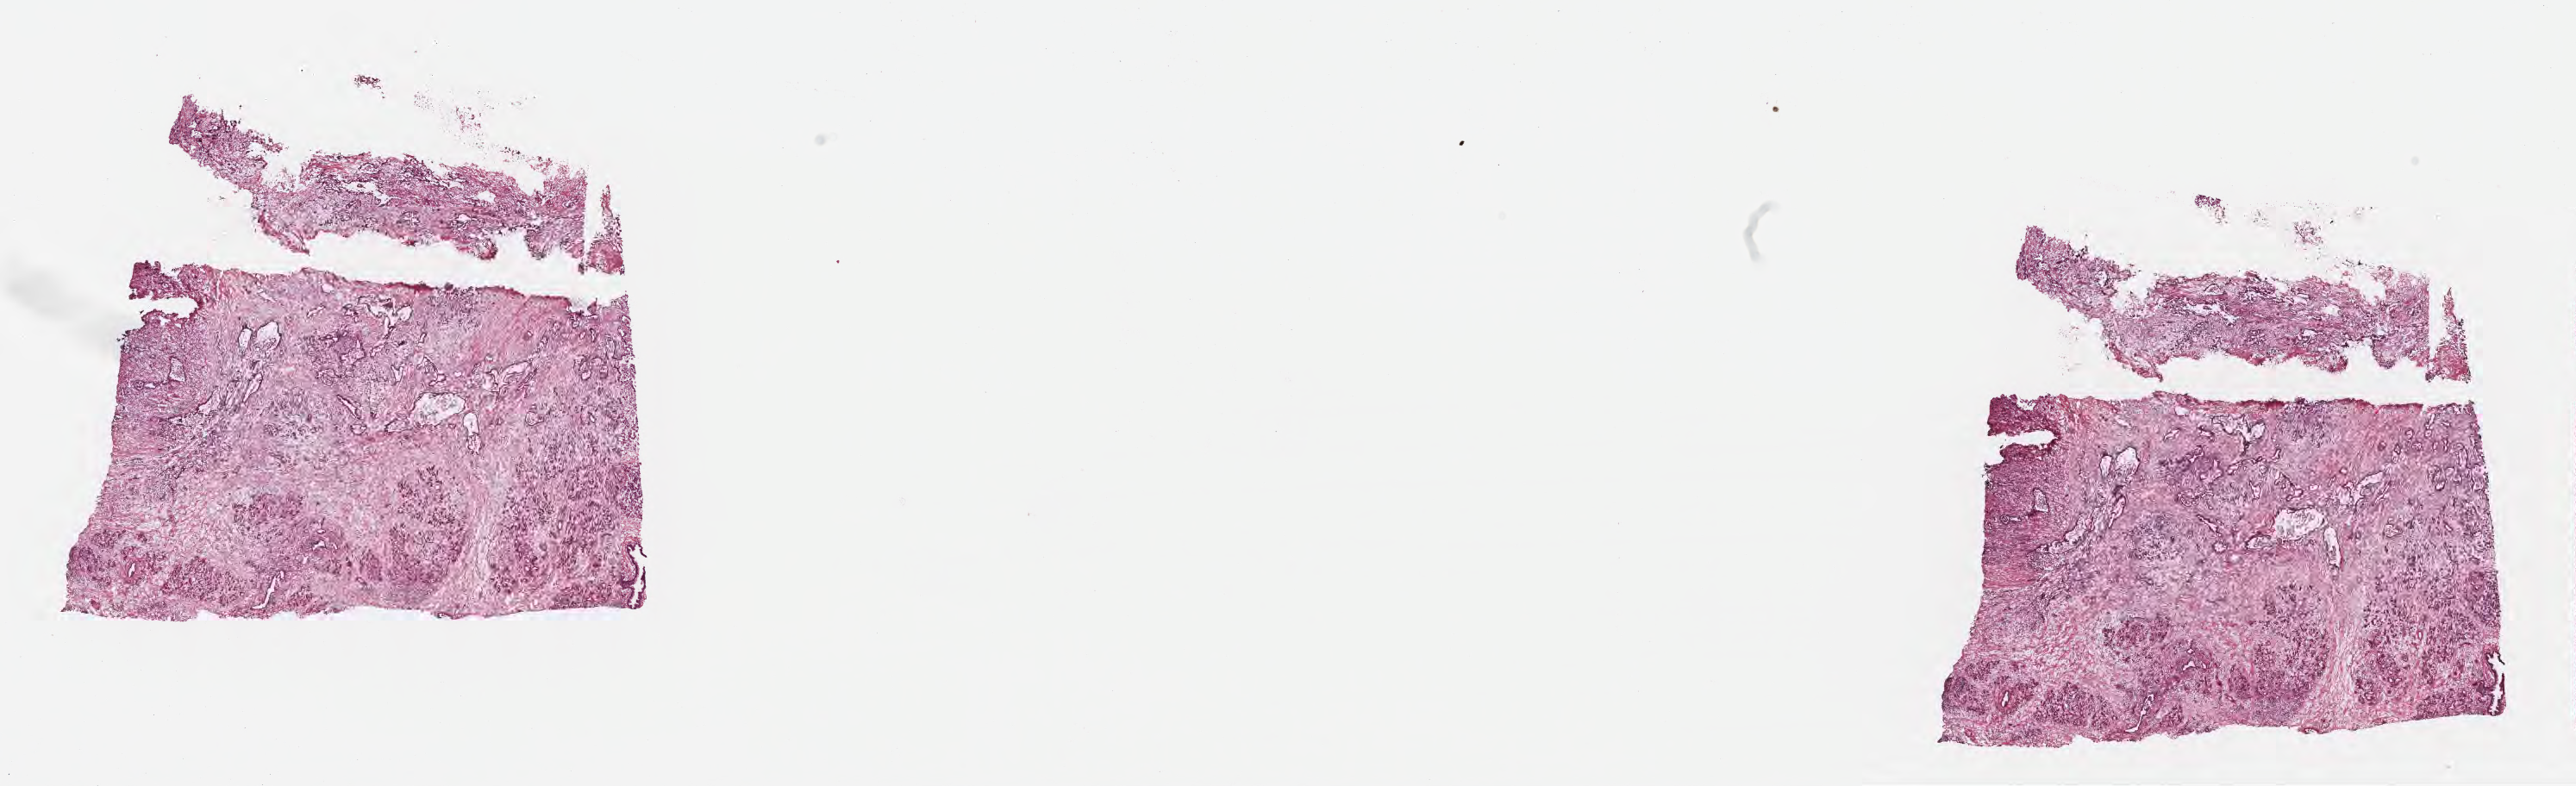
Whole-slide image, haematoxylin and eosin stain — whole scanned area (about 24.1 x 7.4 mm) shown as a low-resolution overview. Frozen section (tissue freezing medium). Primary tumor. Anatomic site: head of pancreas. Female patient; age at initial diagnosis 63 years. Pathologist review of this section (percent, as recorded): tumor cells 40%, tumor nuclei 50%.
Histologic diagnosis: Infiltrating duct carcinoma, NOS.